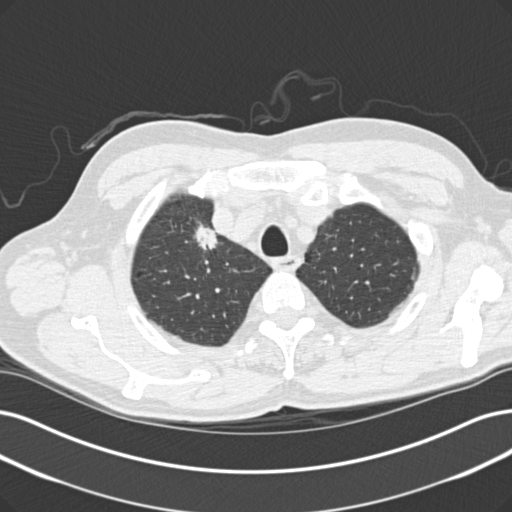
Low-dose screening chest CT, one axial slice. Position 125 of 152 along the scan axis. Lung window (W 1500 / L -600 HU). 2 mm slice thickness. 512 × 512 image matrix, field of view 365 × 365 mm.
Annotated regions visible in this slice (outlined manually by an expert reader):
- lesion 1 (tumor, upper lobe of right lung): bounding box [x1, y1, x2, y2] px = [195, 223, 218, 250]